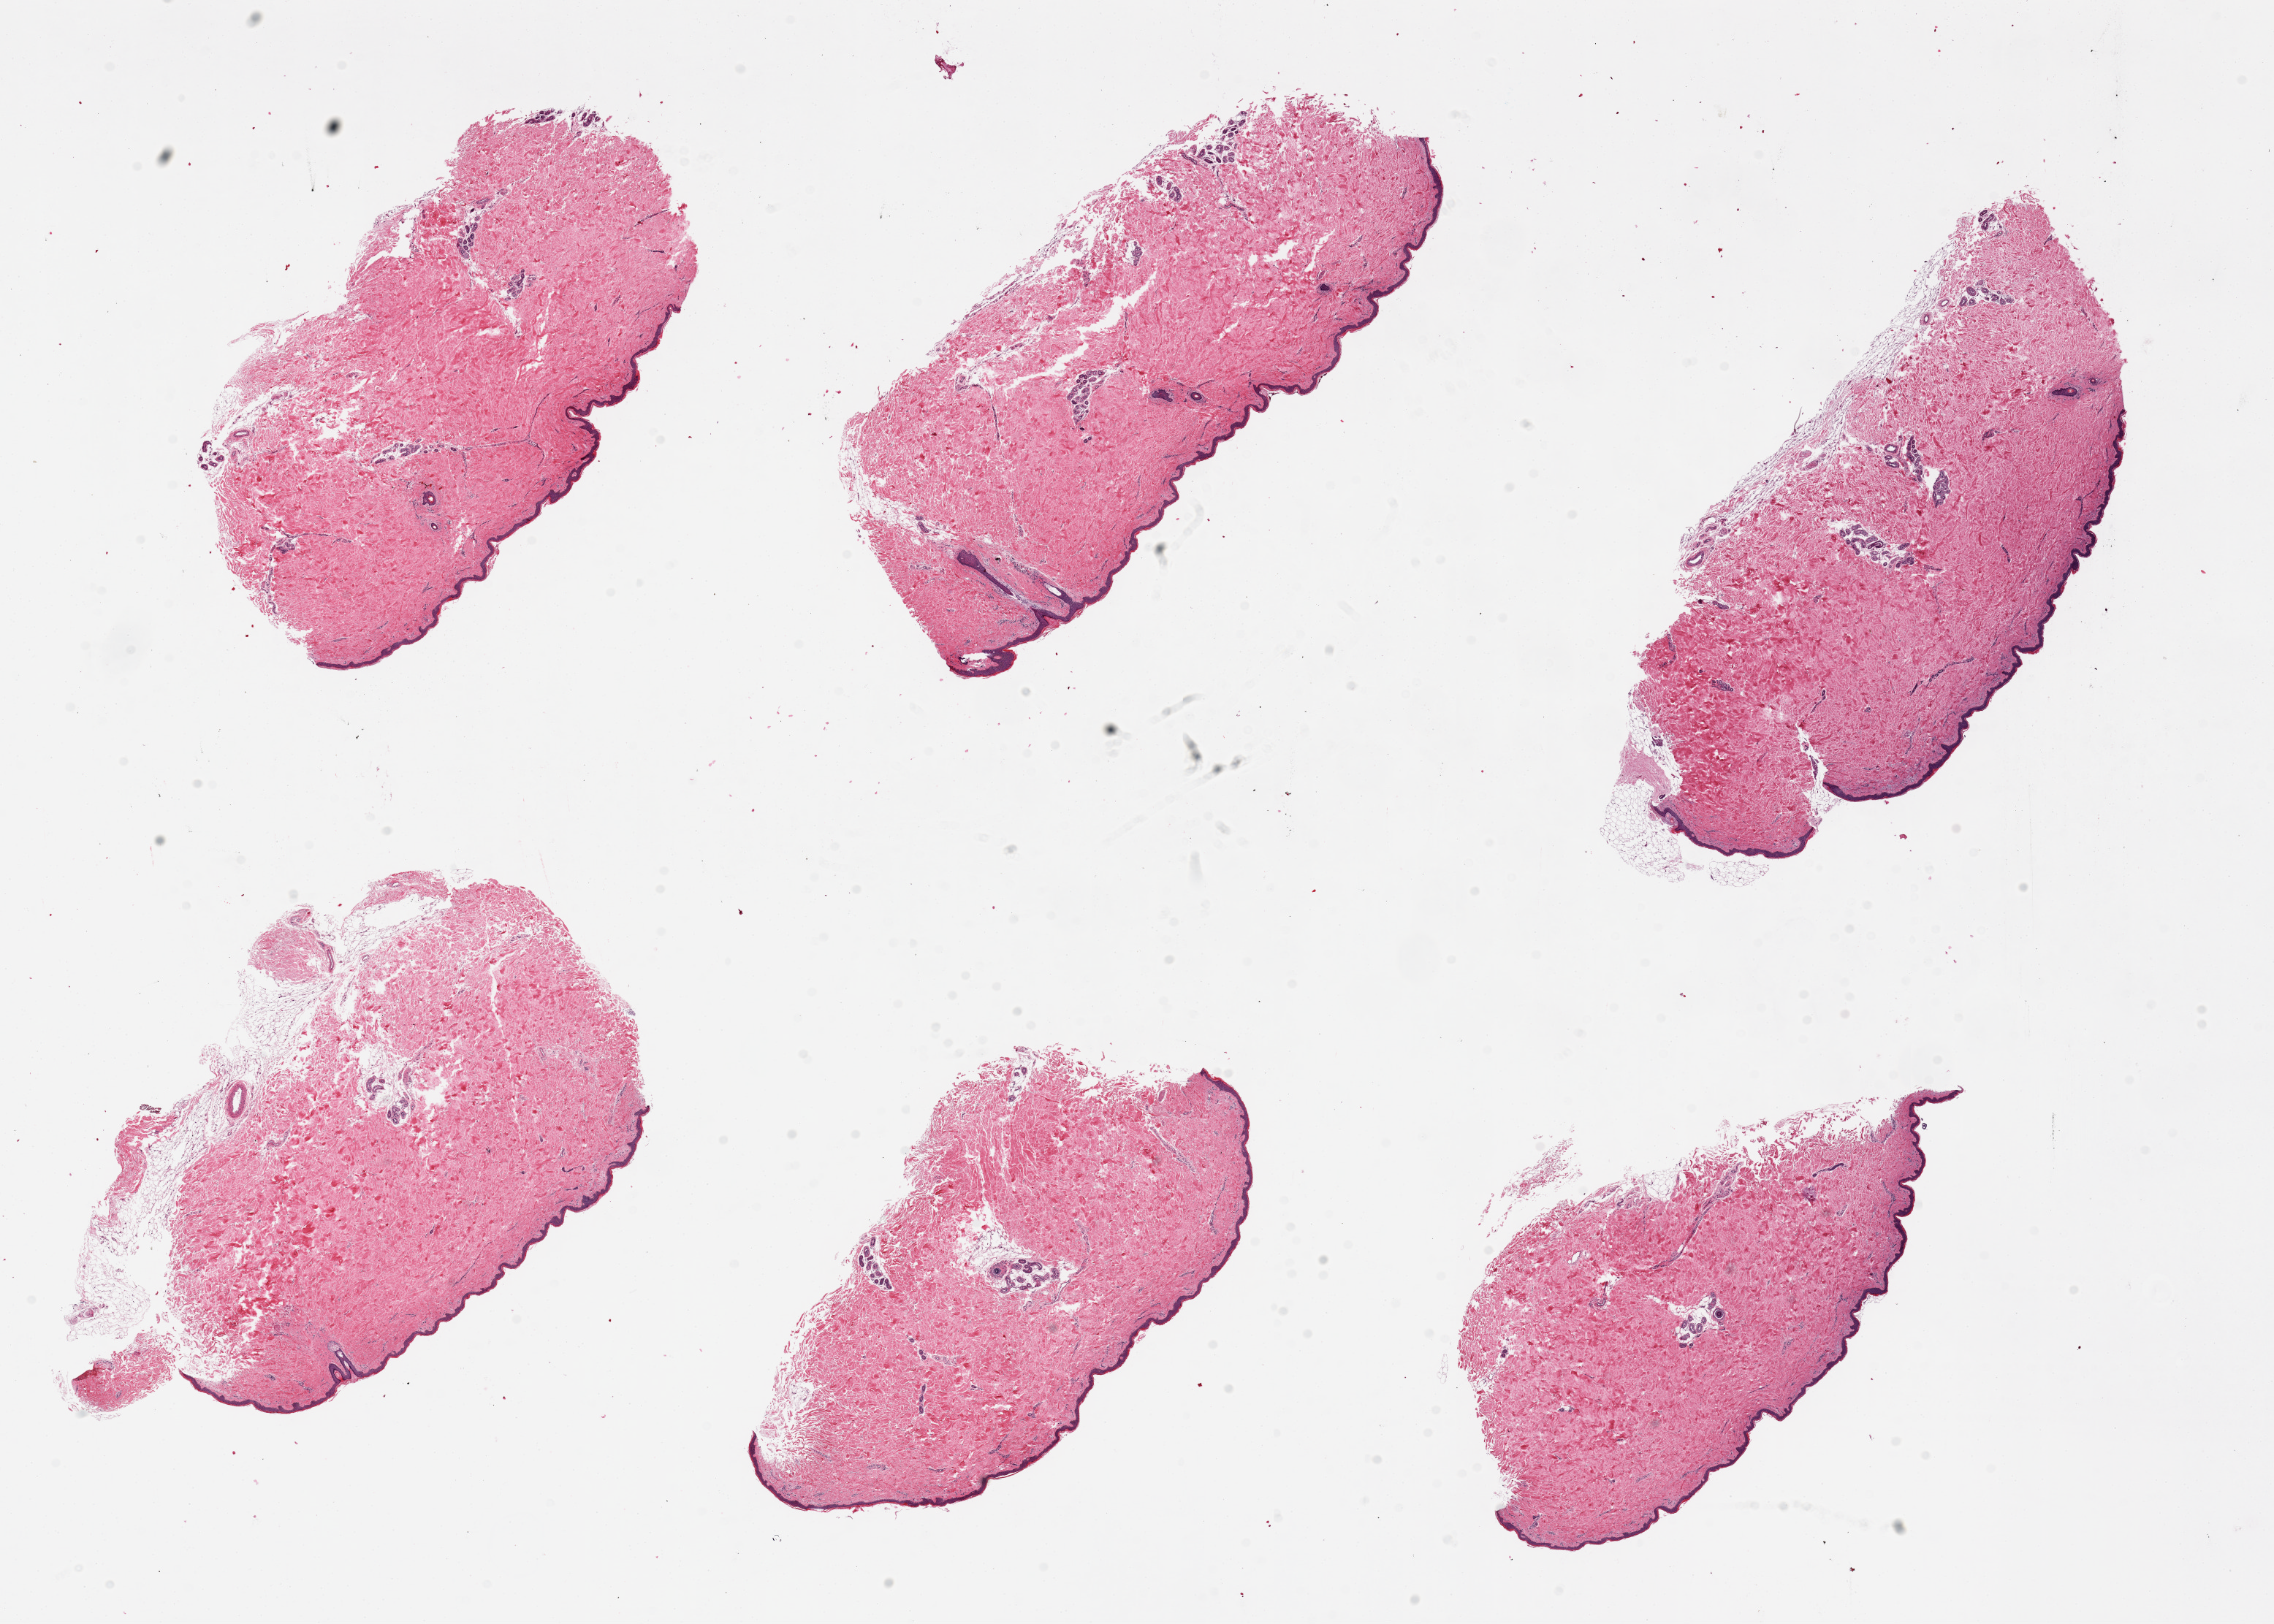
H&E whole-slide image, brightfield — a low-resolution overview of the entire scanned area, about 24.6 x 17.6 mm (acquisition: 20x scan), PAXgene-fixed, paraffin-embedded tissue, sampled site (target tissue): skin of suprapubic region, tissue donor sample.
Review note (as recorded): 6 pieces. up to 8x3.5mm; 5/6 have well trimmed subcutaneous fat.